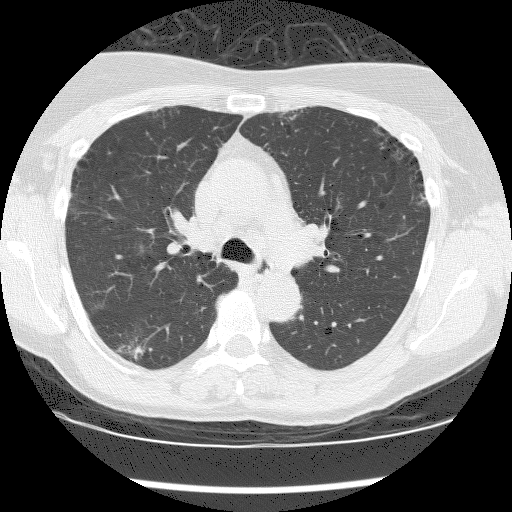
Chest CT (low-dose screening protocol), one axial image, baseline screening round, lung window (W 1500 / L -600 HU), 2.5 mm slice thickness, slice 55 of 176 in the series. Female participant, aged 59 years at enrolment. Current smoker at enrolment.
- Lesion marked by an expert reader, box from (x=111, y=338) to (x=152, y=370) px.
- The screening reader recorded 6 non-calcified nodules or masses ≥4 mm on this exam; which of them this box marks is not recorded.
- Lung cancer was diagnosed 242 days after this screen: adenocarcinoma, NOS, right lower lobe, moderately differentiated (G2), stage IIIA (AJCC 6th edition), 12 mm at pathology.